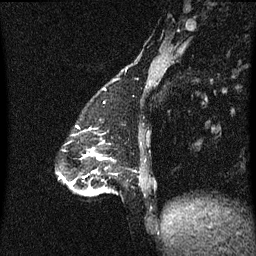
Breast MRI (dynamic contrast-enhanced), one sagittal slice. Dynamic contrast-enhanced series, image 2 of 3 at this slice position (ordered by acquisition). 1.5 T. TE 4.2 ms, TR 8.4 ms. 256 × 256 image matrix, field of view 200 × 200 mm. Female patient, age 47 years.
Annotated regions visible in this slice (semi-automatically segmented with operator editing):
- analysis volume of interest (the breast-tissue region the enhancement analysis was run in; not a lesion): box from (x=81, y=148) to (x=113, y=197) px
- tumour enhancement mask (voxels above the 70 % enhancement threshold inside the analysis volume of interest): (x=91, y=154)–(x=105, y=193)